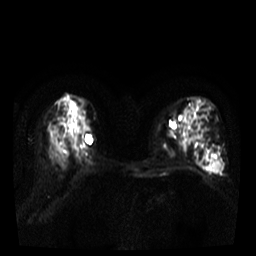
Breast MRI, one axial slice. Slice 20 of 38 in the series (ordered by position). Diffusion-weighted series; image 2 of 4 stored at this slice position (different b-values; order by instance number). 3 T. 5 mm slice thickness. 256 × 256 image matrix, field of view 320 × 320 mm. Female patient.
Structures marked on this image (manually delineated by an expert):
- tumour on diffusion-weighted imaging: bounding box <212,160,221,169> (left, top, right, bottom; pixels)